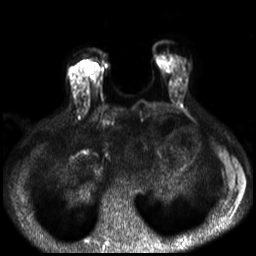
Breast MRI, one axial slice. Slice 9 of 30 in the series (ordered by position). Diffusion-weighted series; image 2 of 4 stored at this slice position (different b-values; order by instance number). 3 T. 4 mm slice thickness. 256 × 256 image matrix, field of view 320 × 320 mm. Female patient.
Outlined on this slice (expert manual segmentation):
- tumour on diffusion-weighted imaging: bounding box <86,68,101,79> (left, top, right, bottom; pixels)